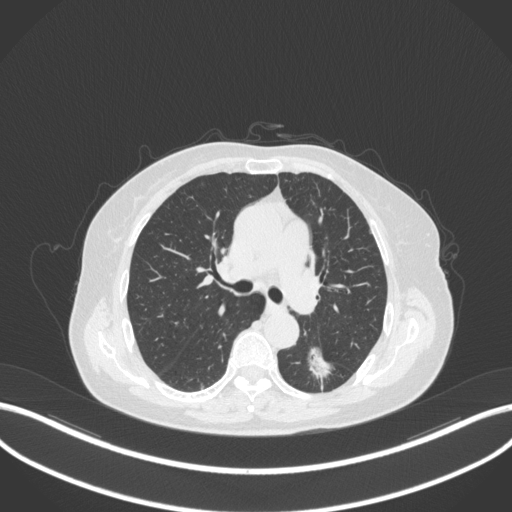
Chest CT, one axial slice; reconstruction kernel B31f; lung window (W 1500 / L -600 HU); 512 × 512 image matrix, field of view 400 × 400 mm. Female patient, age 70 years. Case-level facts recorded for this patient, not image findings: clinical TNM (as recorded): T1c N0 M0.
Outlined on this slice (rectangle marked by the reading radiologist):
- lung tumour (recorded histology: adenocarcinoma): bounding box [x1, y1, x2, y2] px = [301, 340, 341, 385]